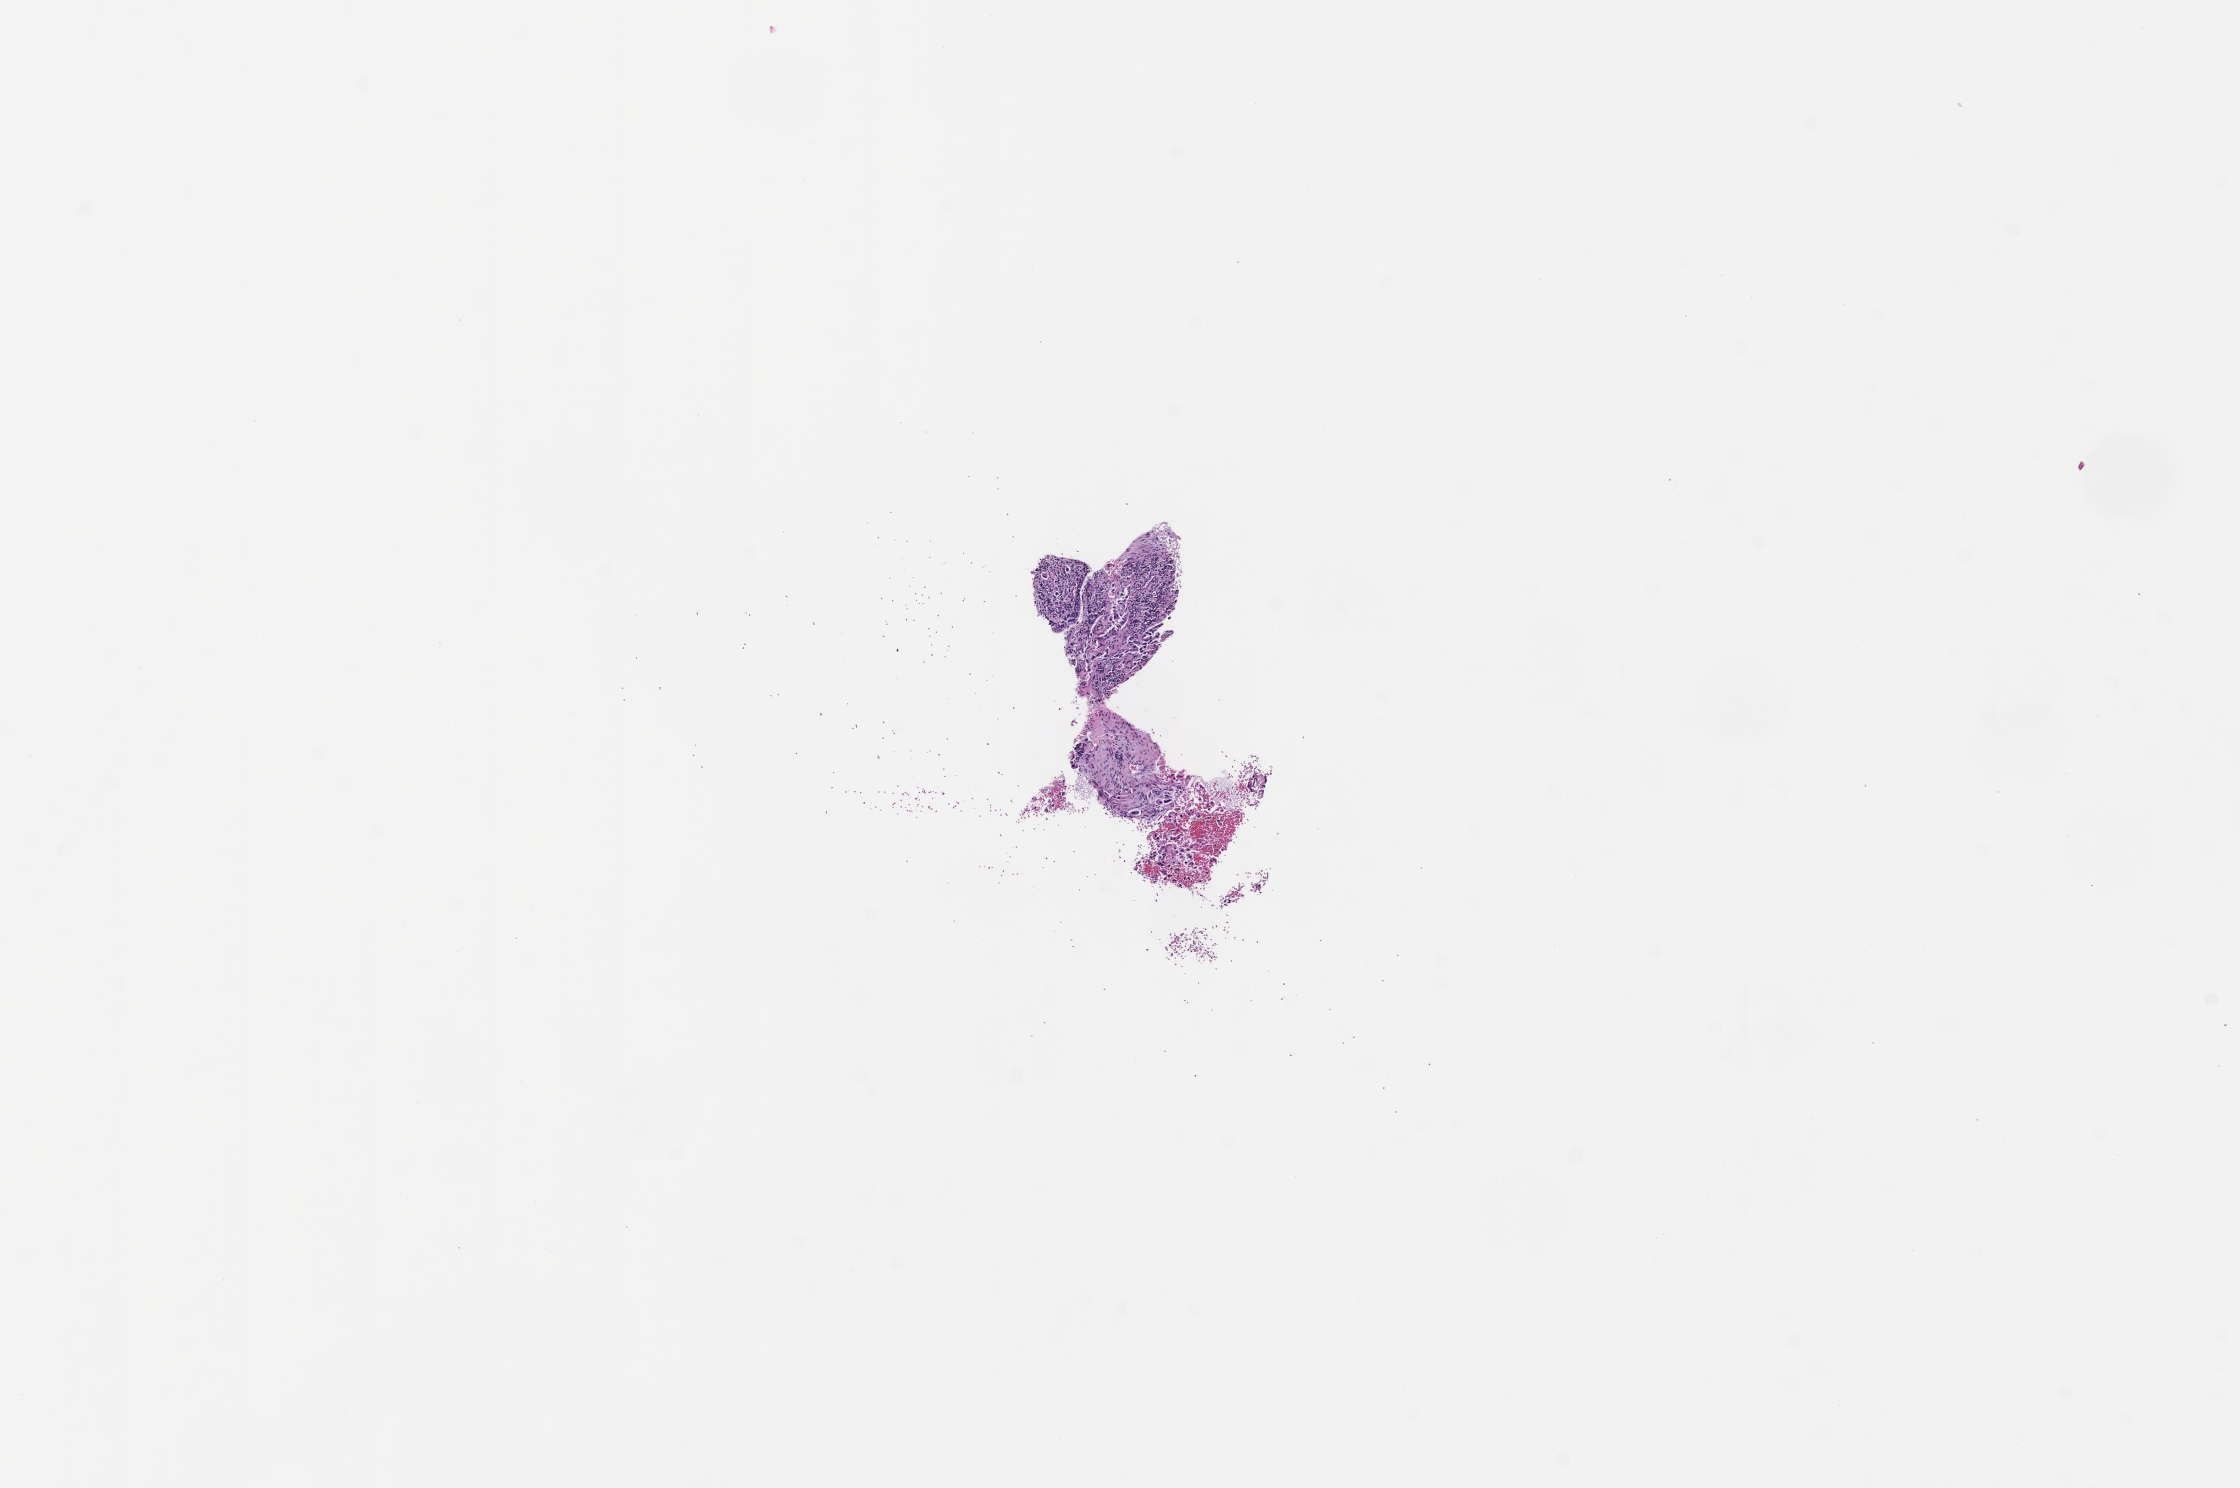
Whole-slide image, hematoxylin and eosin (H&E) stain, shown as a low-resolution overview of the whole scanned area (about 9.0 x 6.0 mm). Formalin-fixed, paraffin-embedded (FFPE) tissue. Site: lung. Specimen time point: collected at baseline (before treatment). Patient: female.
This section: primary tumour tissue. Diagnosis: Non-Small Cell Lung Carcinoma.